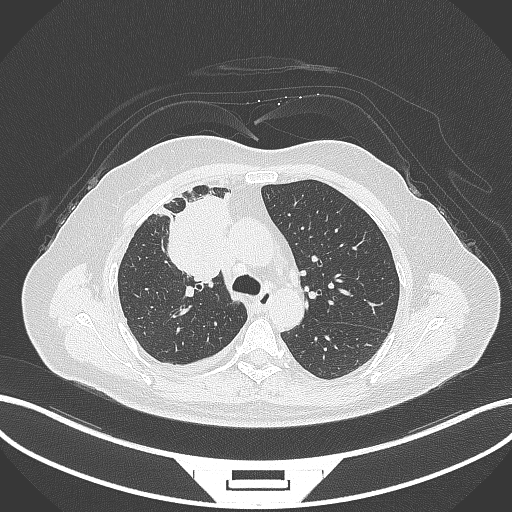
Chest CT, one axial slice; position 194 of 305 along the scan axis; reconstruction kernel B70f; lung window (W 1500 / L -600 HU); 1 mm slice thickness; 512 × 512 image matrix, field of view 400 × 400 mm. Female patient, age 52 years. From the clinical record (not read from this slice): clinical TNM (as recorded): T3 N1 M1.
Annotated regions visible in this slice (rectangle marked by the reading radiologist):
- lung tumour (recorded histology: adenocarcinoma): bounding box [x1, y1, x2, y2] px = [152, 184, 237, 286]